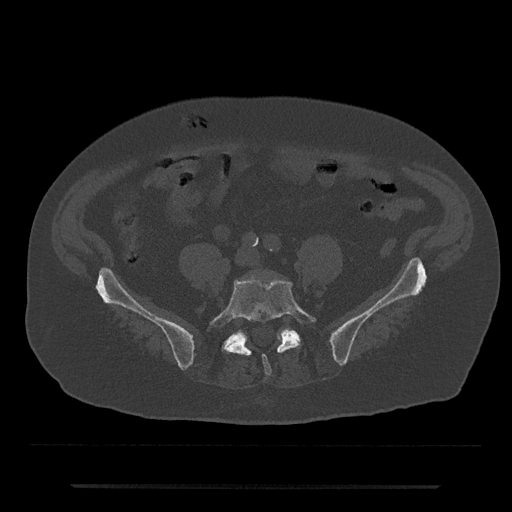
CT including the spine, one axial slice. Slice 283 of 797 in the series (ordered by position). 120 kVp. Bone window (W 1800 / L 400 HU). 0.5 mm slice thickness. 512 × 512 image matrix, field of view 434 × 434 mm. Patient: male, 80 years. From the clinical record (not read from this slice): primary cancer: prostate.
Outlined on this slice (semi-automatically segmented with operator editing):
- L5 vertebra: bounding box <209,277,316,376> (left, top, right, bottom; pixels)